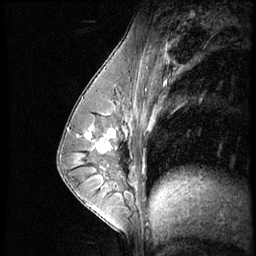
Breast MRI (dynamic contrast-enhanced), one sagittal slice; slice 30 of 56 in the series (ordered by position); dynamic contrast-enhanced series, image 2 of 4 at this slice position (ordered by acquisition); 1.5 T; TE 4.2 ms, TR 8.9 ms; 2.5 mm slice thickness; 256 × 256 image matrix. Patient: female, 35 years. Case-level facts recorded for this patient, not image findings: setting: breast cancer imaged before/during neoadjuvant chemotherapy; receptor status: HER2-positive.
Outlined on this slice (semi-automatic segmentation, software-assisted and operator-edited):
- analysis volume of interest (the breast-tissue region the enhancement analysis was run in; not a lesion): bounding box (x1, y1, x2, y2) in pixels: (73, 111, 131, 164)
- tumour enhancement mask (voxels above the 140 % enhancement threshold inside the analysis volume of interest): (87, 129, 116, 153)